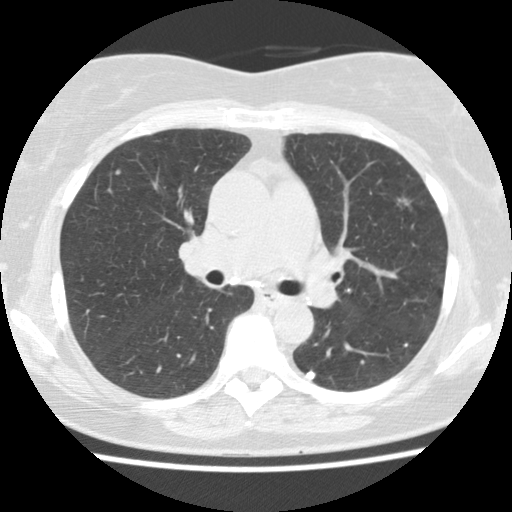
Low-dose screening chest CT, axial slice. Baseline annual screen. Lung window (W 1500 / L -600 HU). Standard (soft-tissue) reconstruction kernel (STANDARD). Slice 52 of 123 in the series. 512 × 512 image matrix. Female participant, aged 60 years at enrolment. Current smoker at enrolment.
Lesion marked by an expert reader, box from (x=377, y=190) to (x=421, y=228) px. The screening reader recorded 2 non-calcified nodules or masses ≥4 mm on this exam (left upper lobe, right upper lobe); which of them this box marks is not recorded. Official screen result: positive, change unspecified: nodule(s) >= 4 mm or enlarging nodule(s), mass(es), or other non-specific abnormalities suspicious for lung cancer. Later outcome: lung cancer diagnosed 388 days after this screen (after the second annual screen) — non-small cell carcinoma, left upper lobe, poorly differentiated (G3), stage IA (AJCC 6th edition), 10 mm at pathology.